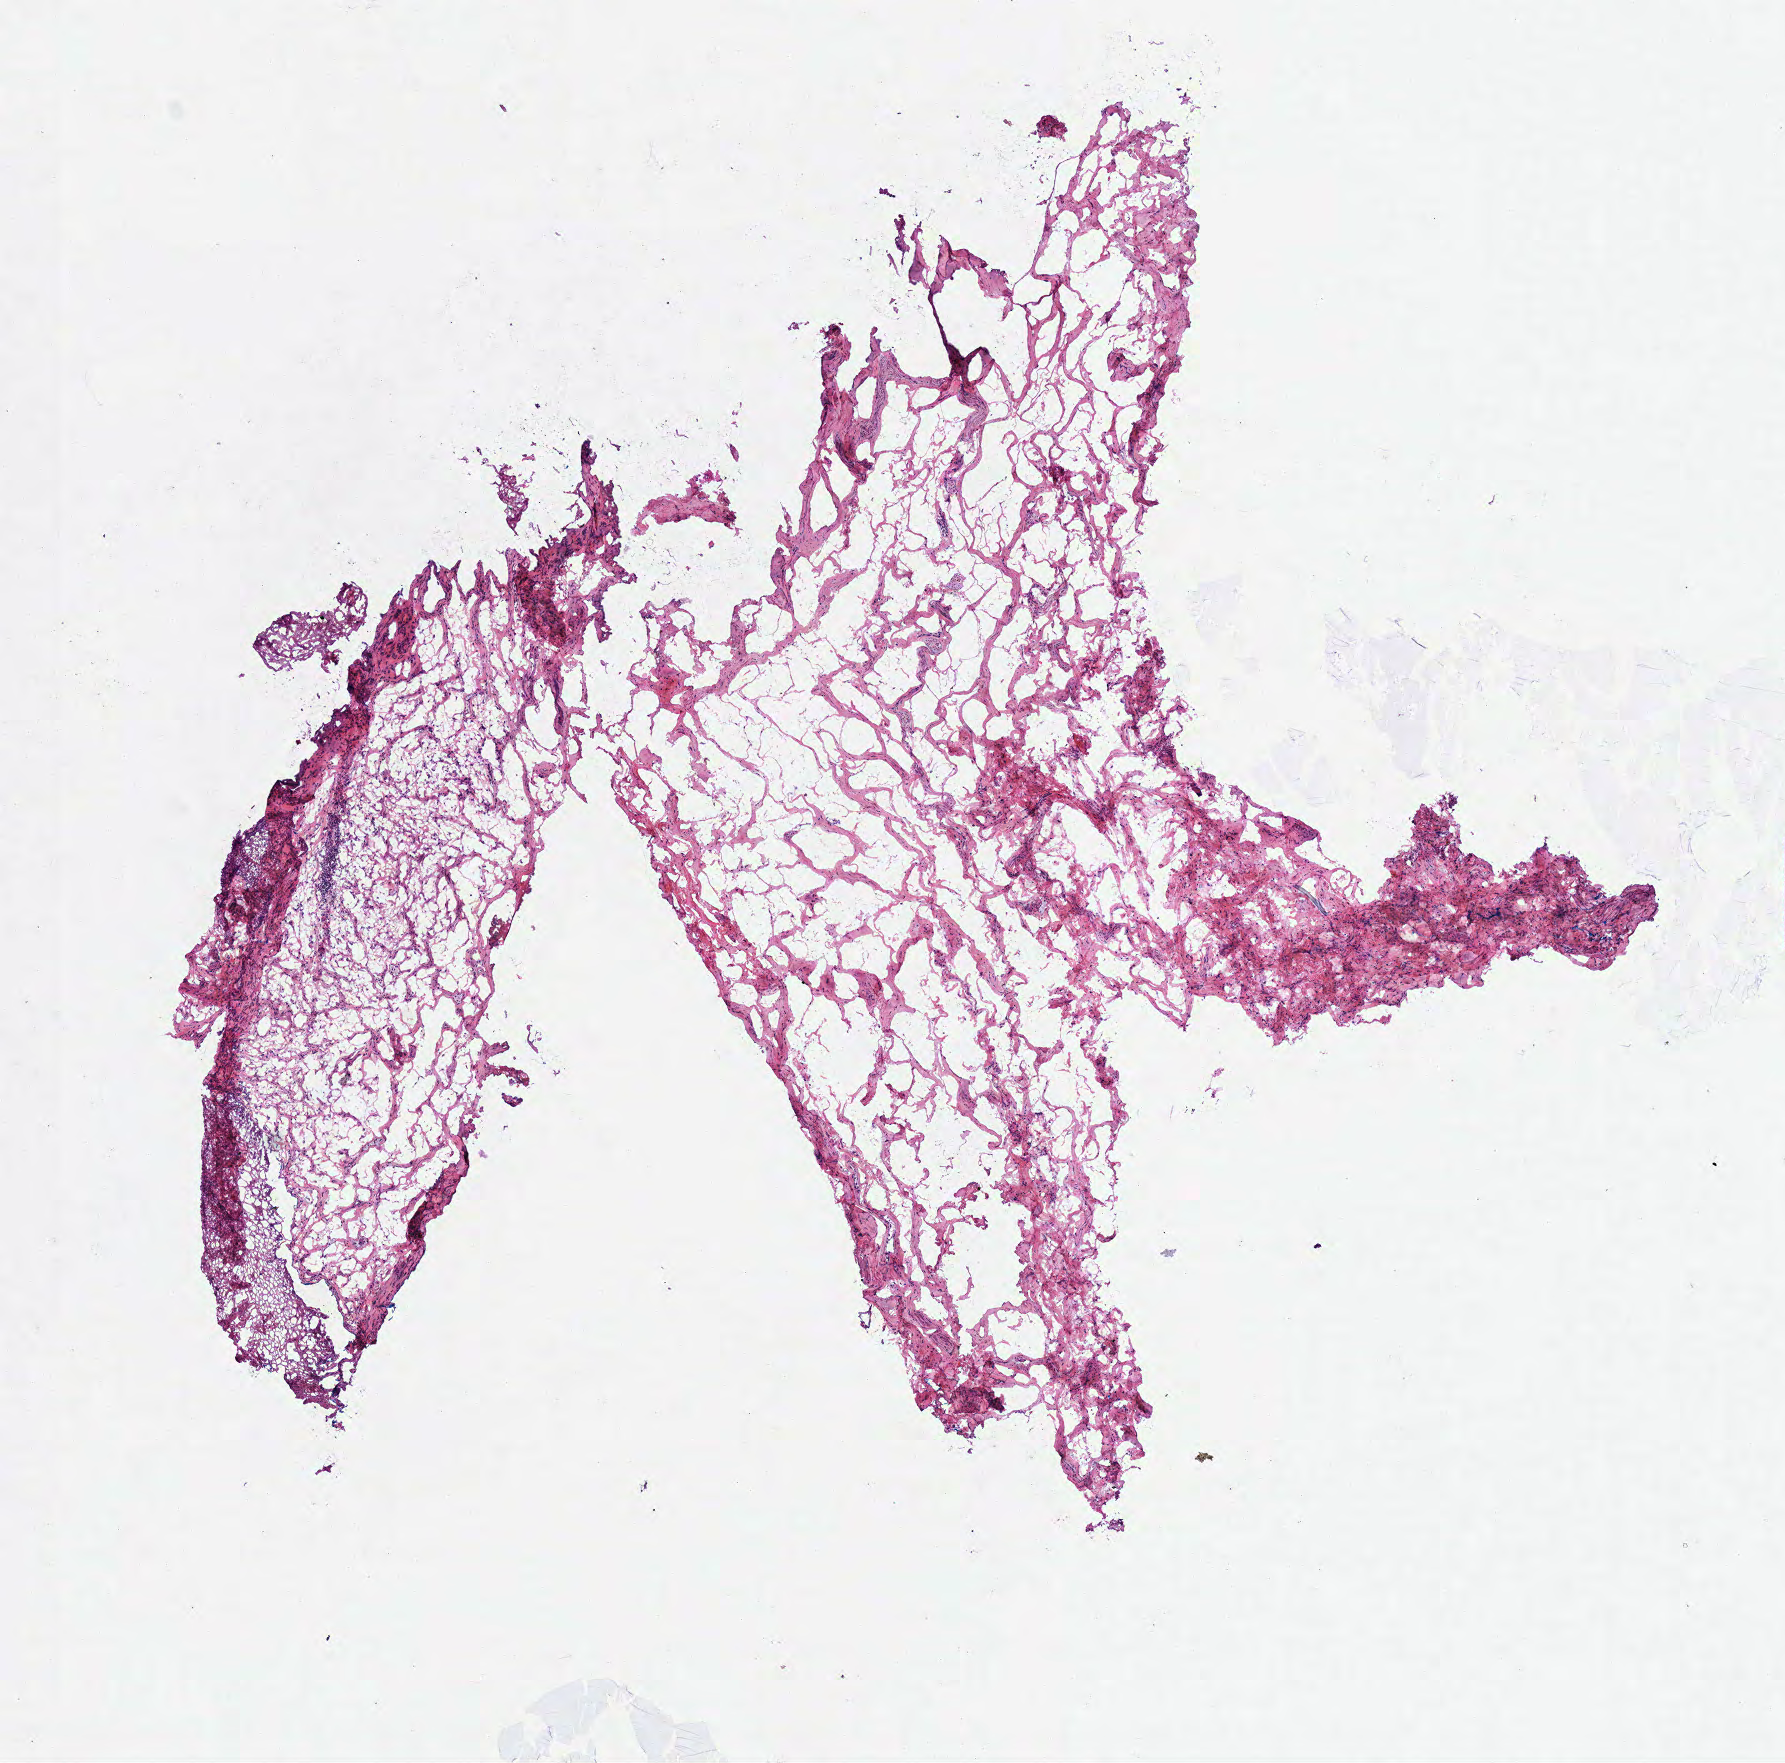
Whole-slide histology image, H&E — low-resolution overview of the scanned area, about 7.0 x 6.9 mm (from a 40x scan). Frozen section. Sample: solid tissue normal (non-tumour tissue), head and neck. Patient: male, age at initial diagnosis 49 years.
• this section: solid tissue normal sample (biorepository sample class)
• patient diagnosis: Squamous cell carcinoma, NOS (overlapping lesion of lip, oral cavity and pharynx)